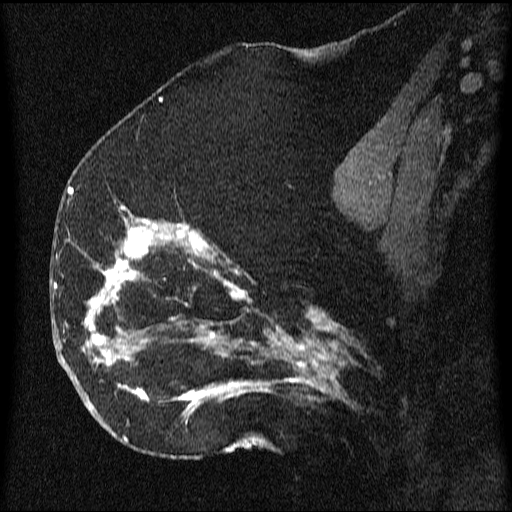
Breast MRI (dynamic contrast-enhanced), one sagittal slice. Position 31 of 64 along the scan axis. Dynamic contrast-enhanced series, image 2 of 3 at this slice position (ordered by acquisition). 1.5 T. TE 4.2 ms, TR 9.1 ms. 512 × 512 image matrix, field of view 180 × 180 mm. Female patient, age 52 years.
Structures marked on this image (semi-automatically segmented with operator editing):
- analysis volume of interest (the breast-tissue region the enhancement analysis was run in; not a lesion): bounding box [x1, y1, x2, y2] px = [61, 203, 350, 438]
- tumour enhancement mask (voxels above the 70 % enhancement threshold inside the analysis volume of interest): [67, 206, 339, 438]